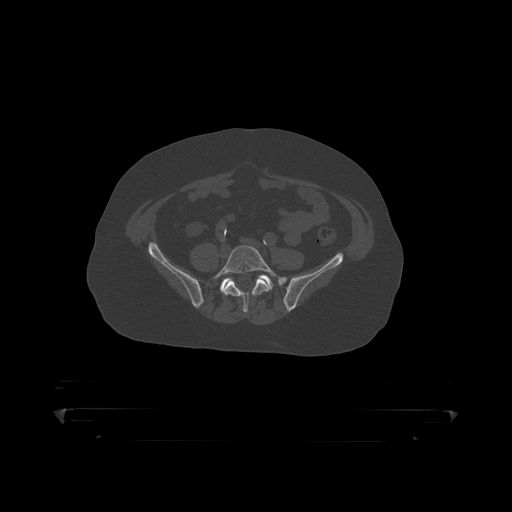
CT including the spine, one axial slice. Slice 37 of 390 in the series (ordered by position). Reconstruction kernel STANDARD. 120 kVp. Bone window (W 1800 / L 400 HU). 512 × 512 image matrix, field of view 650 × 650 mm. Patient: male, 60 years. From the clinical record (not read from this slice): primary cancer: prostate.
Structures marked on this image (semi-automatically segmented with operator editing):
- L5 vertebra: bounding box <210,245,280,314> (left, top, right, bottom; pixels)